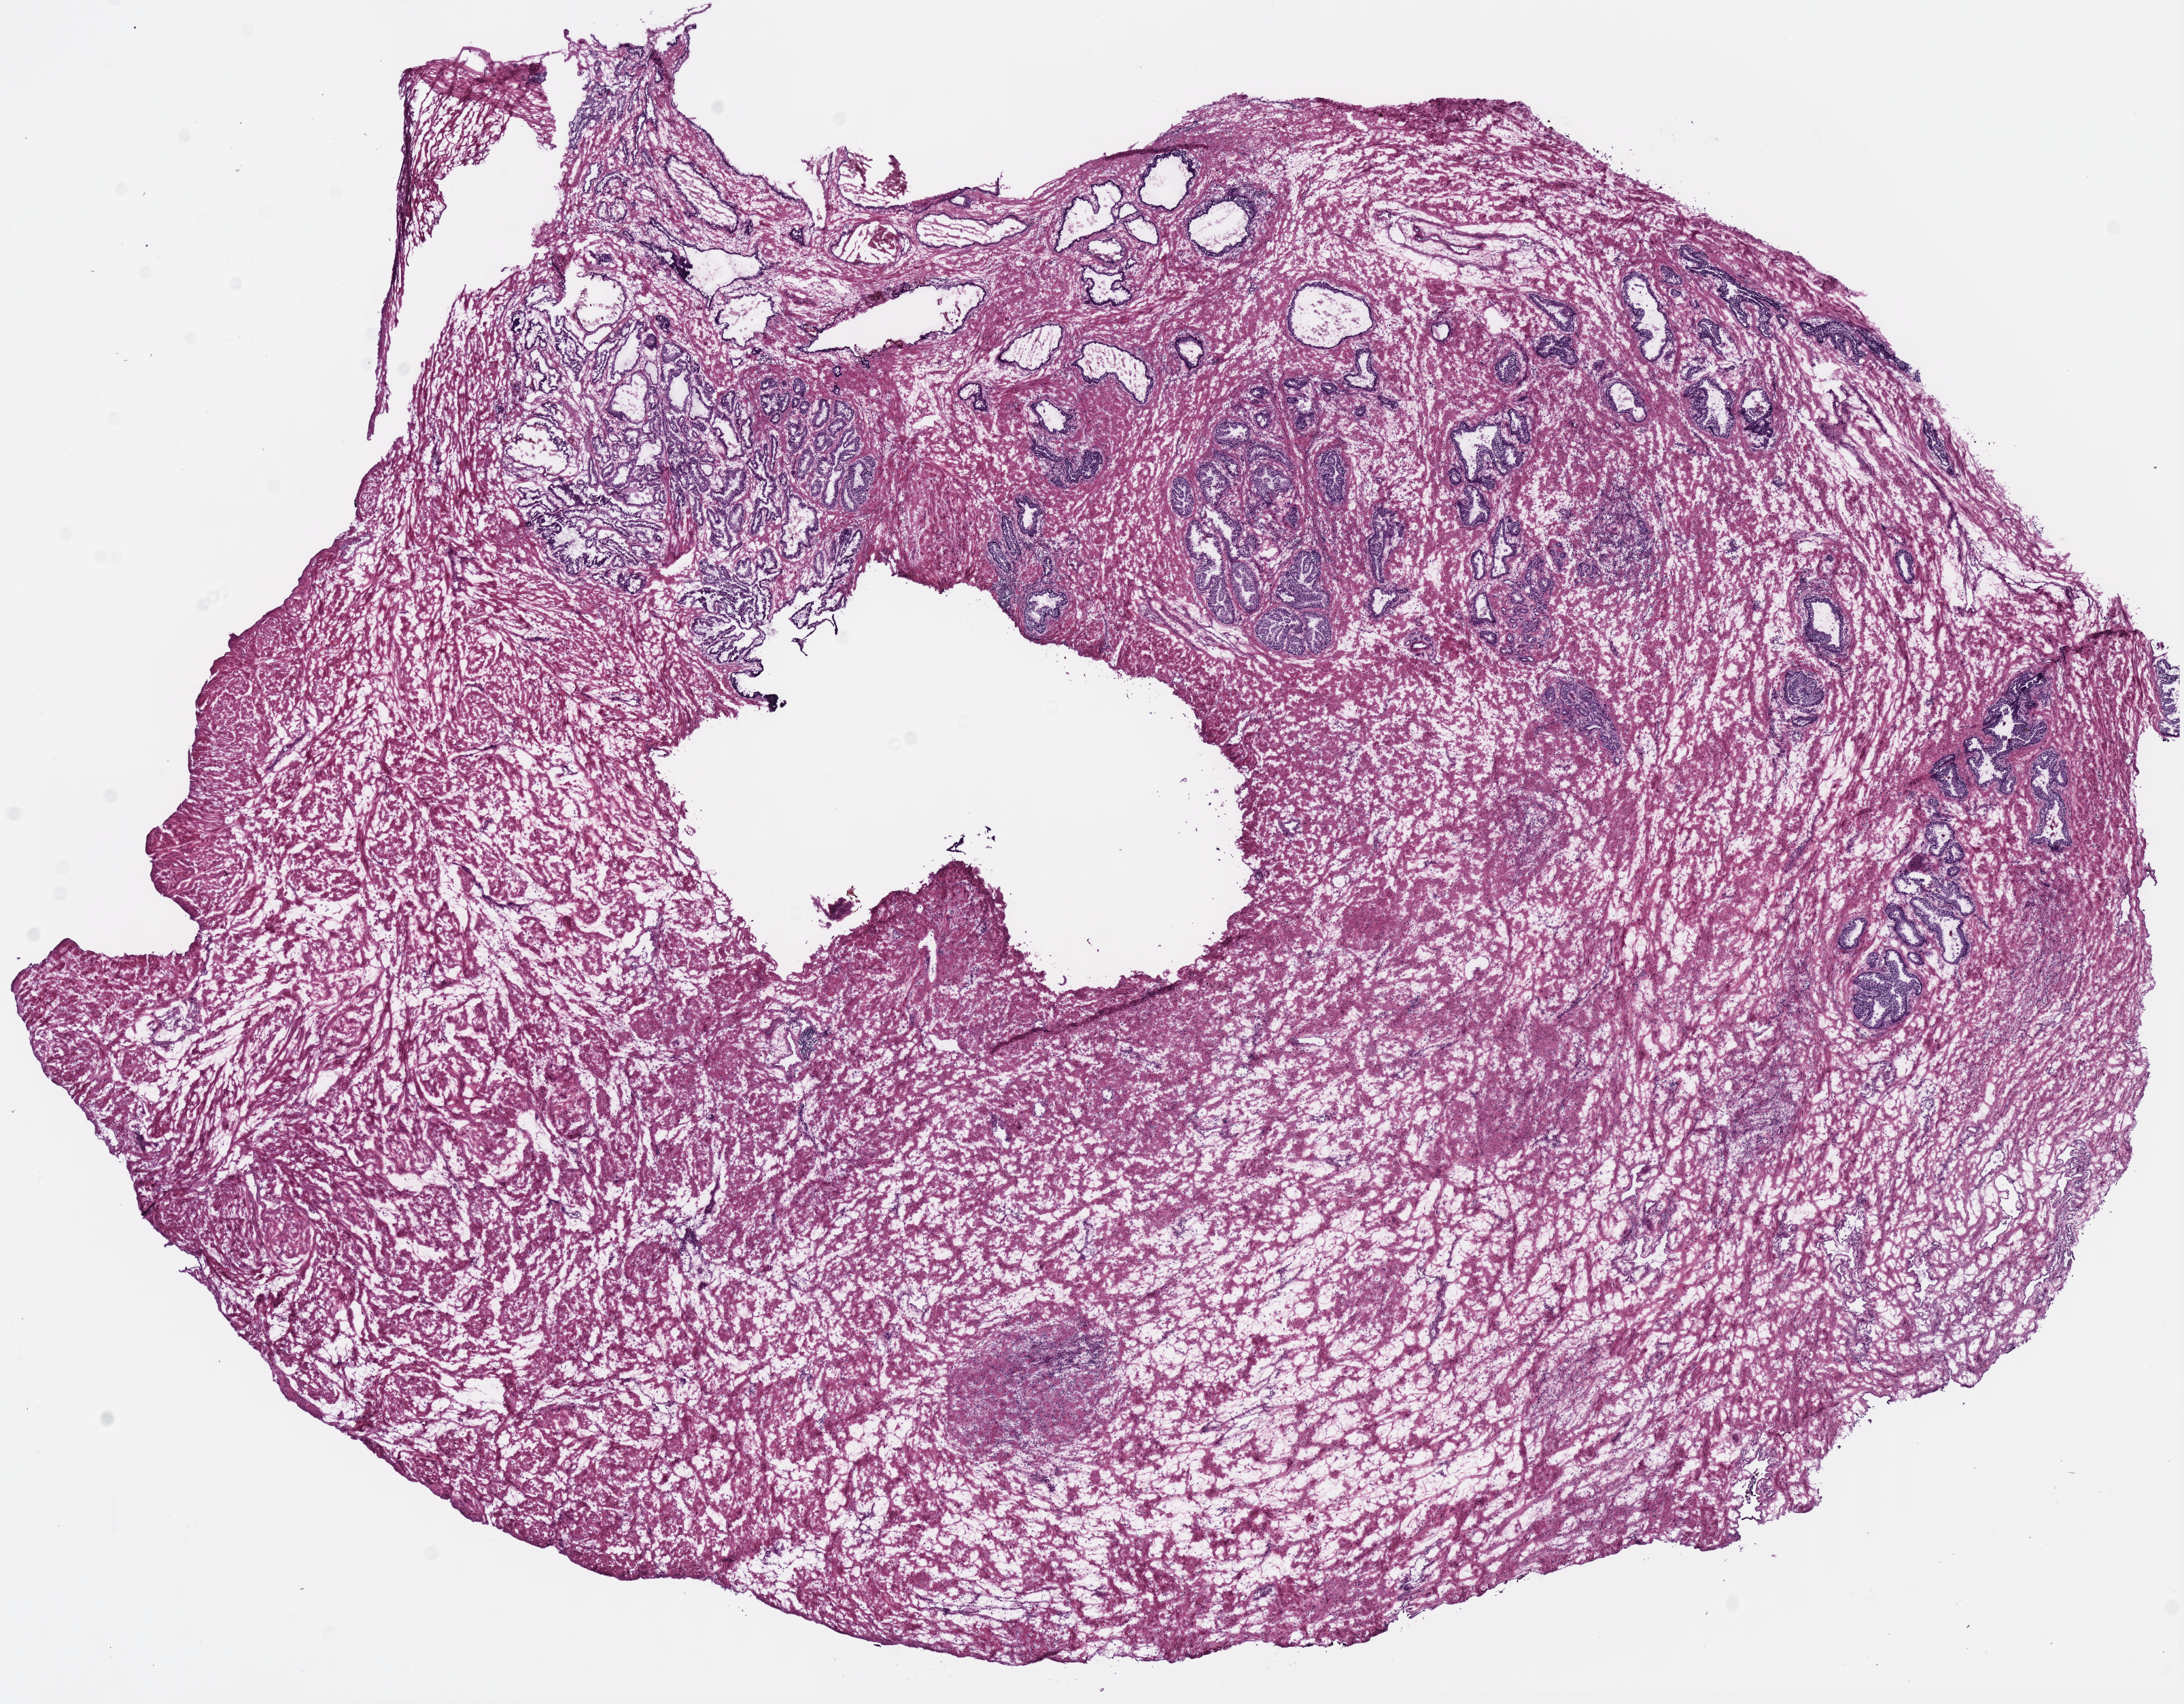
Whole-slide histology image, H&E-stained, shown as a low-resolution overview of the whole scanned area (about 12.7 x 9.9 mm, acquisition: 40x scan); frozen section; sample: solid tissue normal (non-tumour tissue), prostate. Patient: male, age at initial diagnosis 62 years.
- this section: solid tissue normal (non-tumour) sample from the same patient
- patient diagnosis: Acinar cell carcinoma (prostate gland)